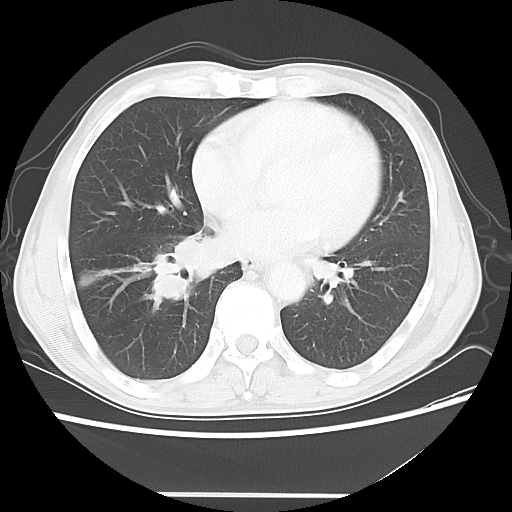
Chest CT, one axial slice; slice 22 of 56 in the series (ordered by position); reconstruction kernel LUNG; 120 kVp; lung window (W 1500 / L -600 HU); 5 mm slice thickness; 512 × 512 image matrix. Male patient, age 65 years. From the clinical record (not read from this slice): clinical TNM (as recorded): T1c N3 M0.
Structures marked on this image (bounding box drawn by a radiologist):
- lung tumour (recorded histology: small cell carcinoma): bounding box (x1, y1, x2, y2) in pixels: (140, 227, 238, 304)